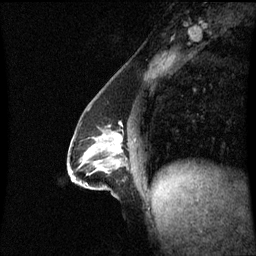
Breast MRI (dynamic contrast-enhanced), one sagittal slice. Position 30 of 60 along the scan axis. Dynamic contrast-enhanced series, image 2 of 3 at this slice position (ordered by acquisition). 1.5 T. TE 4.2 ms, TR 8.9 ms. 2.2 mm slice thickness. 256 × 256 image matrix. Female patient, age 47 years. From the clinical record (not read from this slice): setting: breast cancer imaged before/during neoadjuvant chemotherapy; receptor status: HR-positive, HER2-negative.
Annotated regions visible in this slice (semi-automatic segmentation, software-assisted and operator-edited):
- analysis volume of interest (the breast-tissue region the enhancement analysis was run in; not a lesion): bounding box [x1, y1, x2, y2] px = [69, 128, 128, 196]
- tumour enhancement mask (voxels above the 70 % enhancement threshold inside the analysis volume of interest): [111, 134, 120, 154]